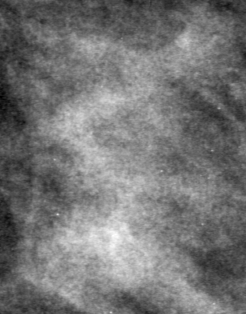
Crop from a digitized film mammogram around one marked abnormality; right breast; MLO view.
Mass, shape focal asymmetric density, margins ill defined; BI-RADS assessment category 4; subtlety rating 4 on a 1 (subtle) to 5 (obvious) scale; pathology result (as recorded, not read from the image): benign.